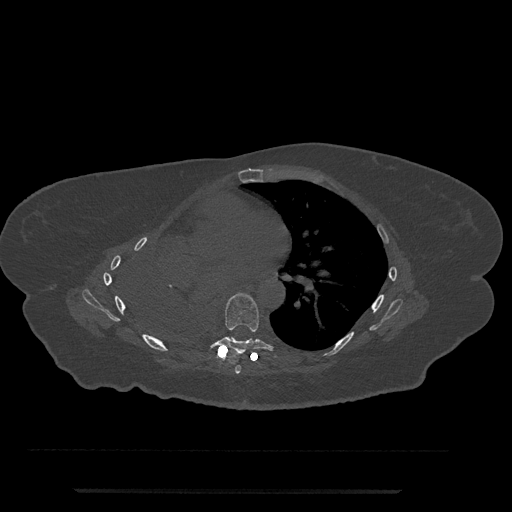
CT including the spine, one axial slice. Slice 444 of 797 in the series (ordered by position). Bone window (W 1800 / L 400 HU). 0.5 mm slice thickness. 512 × 512 image matrix, field of view 440 × 440 mm. Patient: female, 51 years. Case-level facts recorded for this patient, not image findings: primary cancer: neuro.
Structures marked on this image (semi-automatically segmented with operator editing):
- T6 vertebra: bounding box (x1, y1, x2, y2) in pixels: (235, 365, 241, 374)
- T7 vertebra: (207, 293, 278, 356)